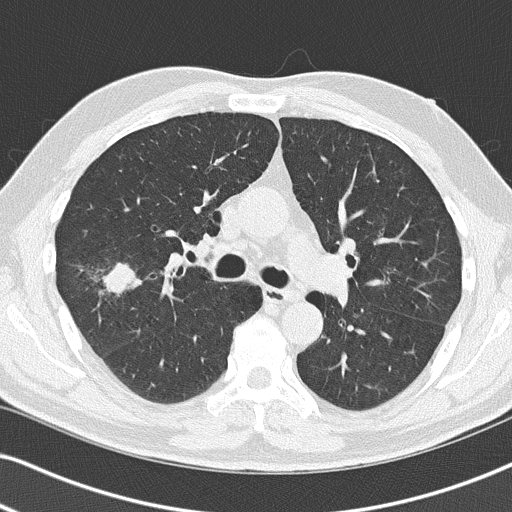
Low-dose screening chest CT, one axial slice. Slice 81 of 140 in the series (ordered by position). Reconstruction kernel B50f. Lung window (W 1500 / L -600 HU). 2 mm slice thickness. 512 × 512 image matrix, field of view 330 × 330 mm.
Outlined on this slice (expert manual segmentation):
- lesion 1 (tumor, upper lobe of right lung): box from (x=102, y=263) to (x=142, y=296) px